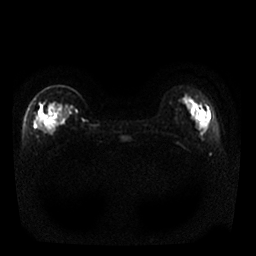
Breast MRI, one axial slice; position 5 of 25 along the scan axis; diffusion-weighted series; image 2 of 4 stored at this slice position (different b-values; order by instance number); 1.5 T; 4 mm slice thickness; 256 × 256 image matrix. Female patient.
Structures marked on this image (expert manual segmentation):
- tumour on diffusion-weighted imaging: box from (x=38, y=112) to (x=43, y=128) px